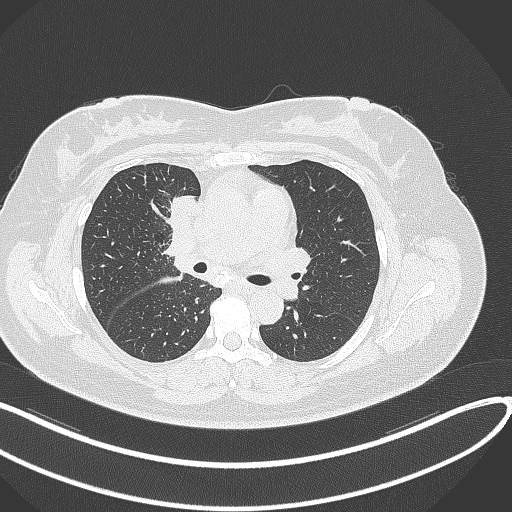
Chest CT, one axial slice. Slice 161 of 303 in the series (ordered by position). Lung window (W 1500 / L -600 HU). 512 × 512 image matrix, field of view 400 × 400 mm. Female patient, age 46 years. From the clinical record (not read from this slice): clinical TNM (as recorded): T2a N1 M0.
Annotated regions visible in this slice (rectangle marked by the reading radiologist):
- lung tumour (recorded histology: adenocarcinoma): box from (x=165, y=193) to (x=198, y=232) px